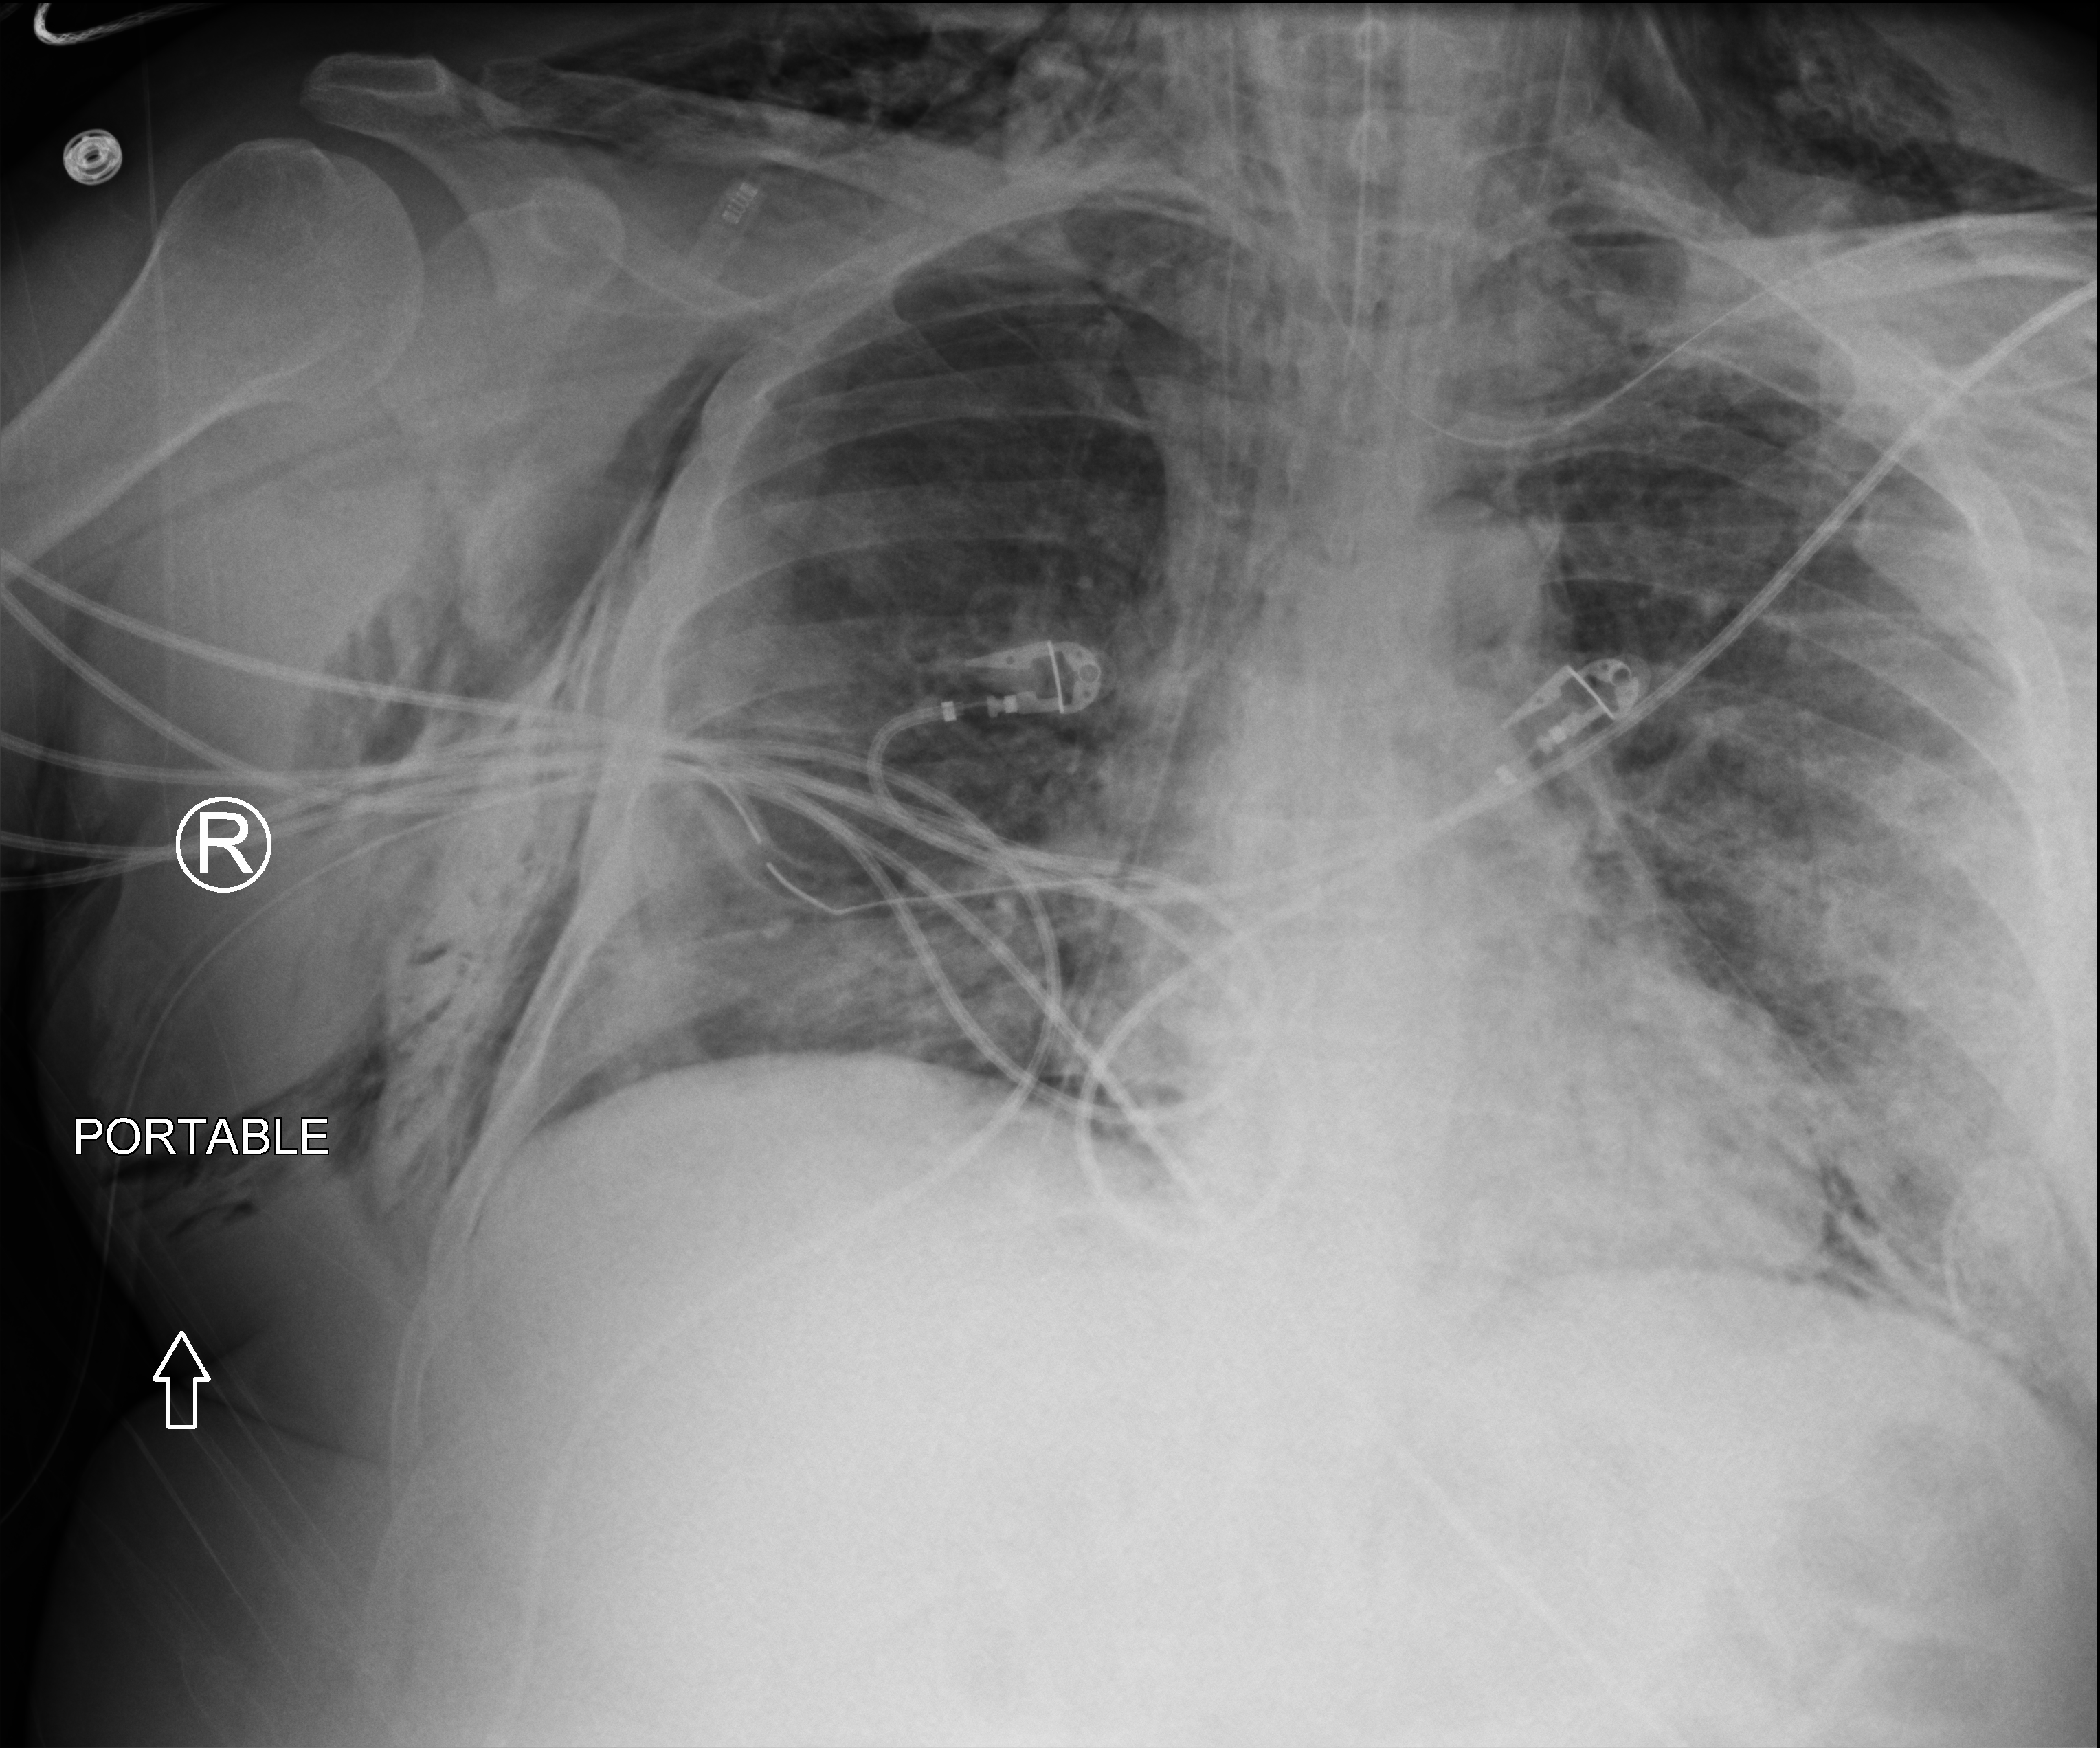
Bedside chest radiograph (computed radiography); anteroposterior (AP) projection. Patient hospitalised with COVID-19; male, aged 18–59 years.
From the hospital-stay record, not from the radiograph (when in the stay this image was taken is not recorded):
- hypertension (admission record): yes
- mechanically ventilated during this hospital stay: yes